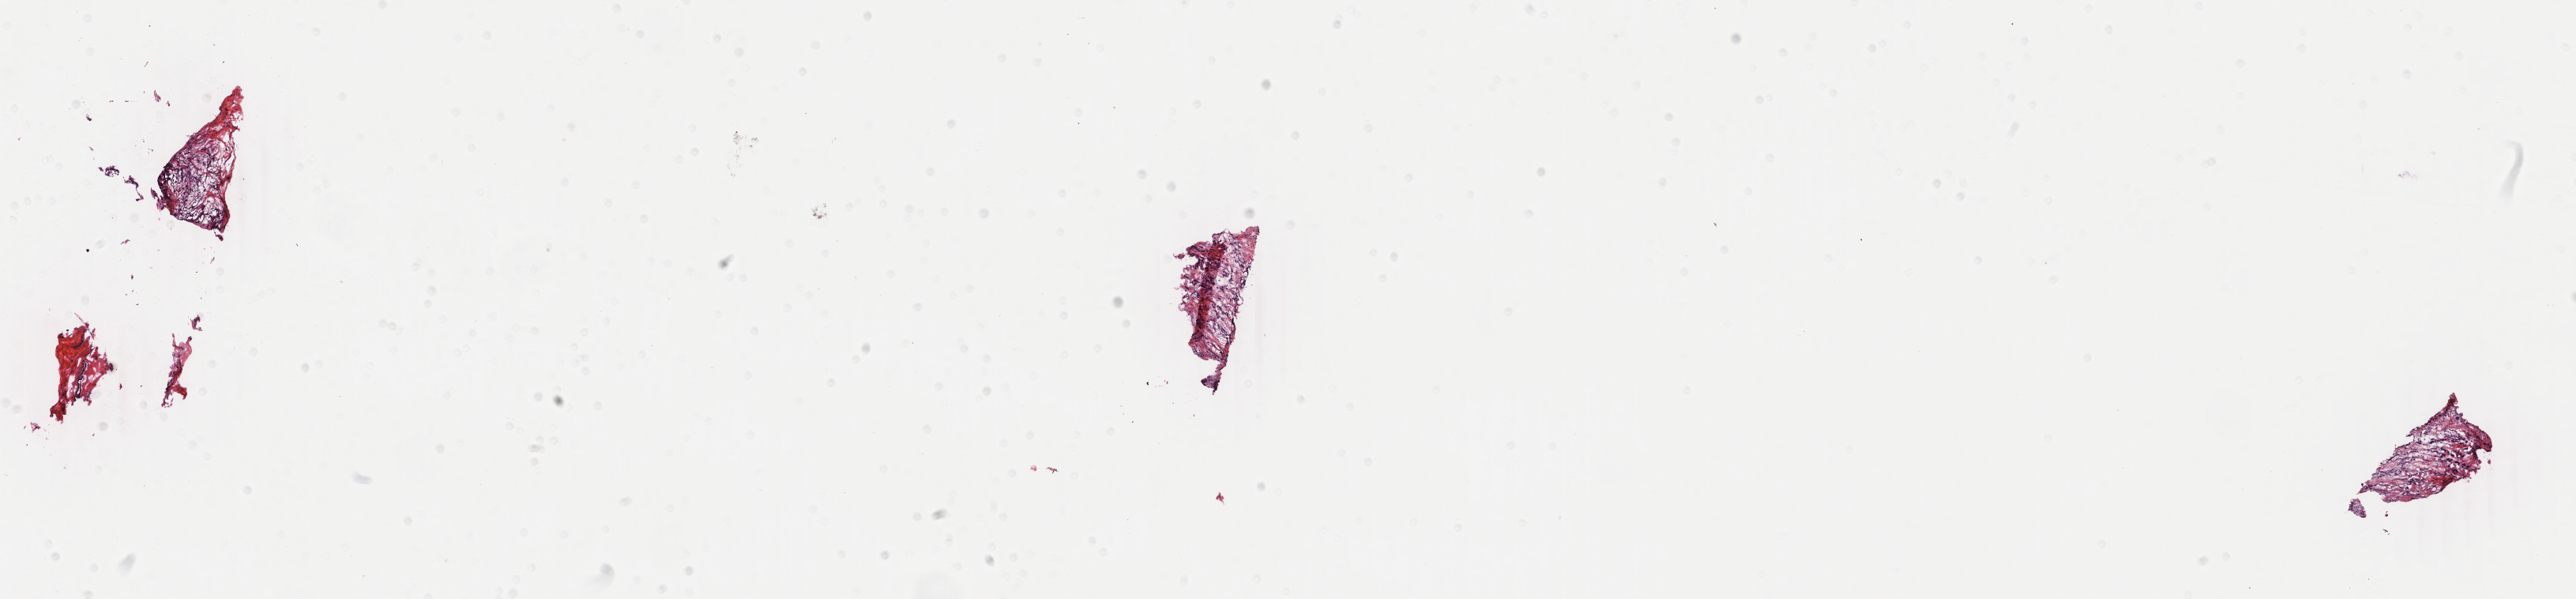
Whole-slide histology image, H&E, low-resolution overview of the scanned area, about 25.9 x 6.0 mm; frozen section; breast, primary tumour sample. Female, age 71 years at initial diagnosis. Slide review estimates, as recorded: tumour cells 49%, tumour nuclei 70%, normal cells 40%, stromal cells 10%, necrosis 1%. Inflammatory infiltration, as recorded: lymphocyte infiltration 2%, monocyte infiltration 0%, neutrophil infiltration 0%.
TNM: T2 N0 (i-) M0. AJCC pathologic stage: IIA. Histologic diagnosis: Infiltrating duct carcinoma, NOS. Lymph nodes positive (case pathology): 0 of 2 examined.